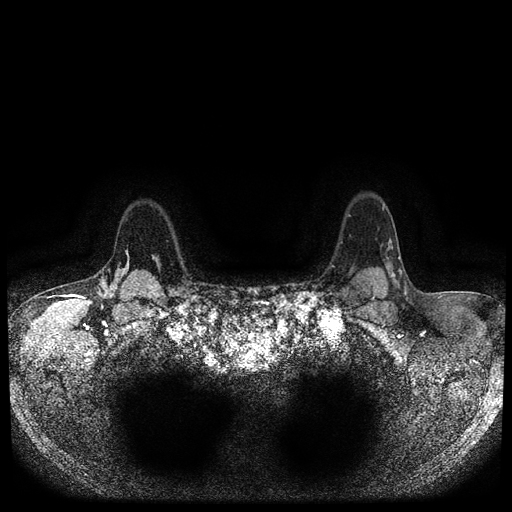
Breast MRI (dynamic contrast-enhanced, multi-phase), one axial slice. Slice 83 of 116 in the series (ordered by position). Dynamic contrast-enhanced series, time point 2 of 5 at this slice position (early post-contrast). 1.5 T. TE 2.6 ms, TR 5.4 ms. 512 × 512 image matrix, field of view 340 × 340 mm. Patient: female, 47 years.
Structures marked on this image (semi-automatic segmentation, software-assisted and operator-edited):
- breast lesion (labelled 'tumour' in the annotation; benign lesions carry a separate 'benign' label): bounding box [x1, y1, x2, y2] px = [151, 254, 163, 272]